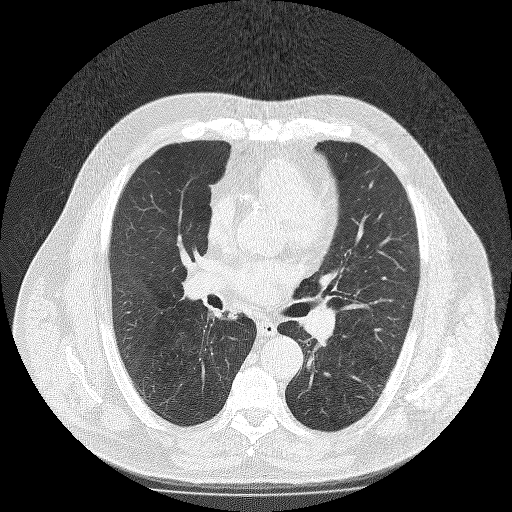
Axial slice from a low-dose chest CT screening exam. Second annual screen. Lung window (W 1500 / L -600 HU). Lung (sharp) reconstruction kernel (FC51). Slice 83 of 188 in the series. 512 × 512 image matrix, field of view 420 × 420 mm. Male, age 65 years at enrolment.
Expert reader's lesion annotation, bounding box [x1, y1, x2, y2] px = [209, 300, 252, 332]. Screening reader's record for this exam (one nodule recorded; not confirmed to be the boxed lesion): non-calcified nodule or mass ≥4 mm, right lower lobe, 10 × 9 mm, spiculated (stellate) margins, soft tissue attenuation, pre-existing on the prior screen: yes; interval growth: no. Lung cancer was diagnosed 247 days after this screen: large cell neuroendocrine carcinoma, right lower lobe, undifferentiated (G4), stage IIIA (AJCC 6th edition).